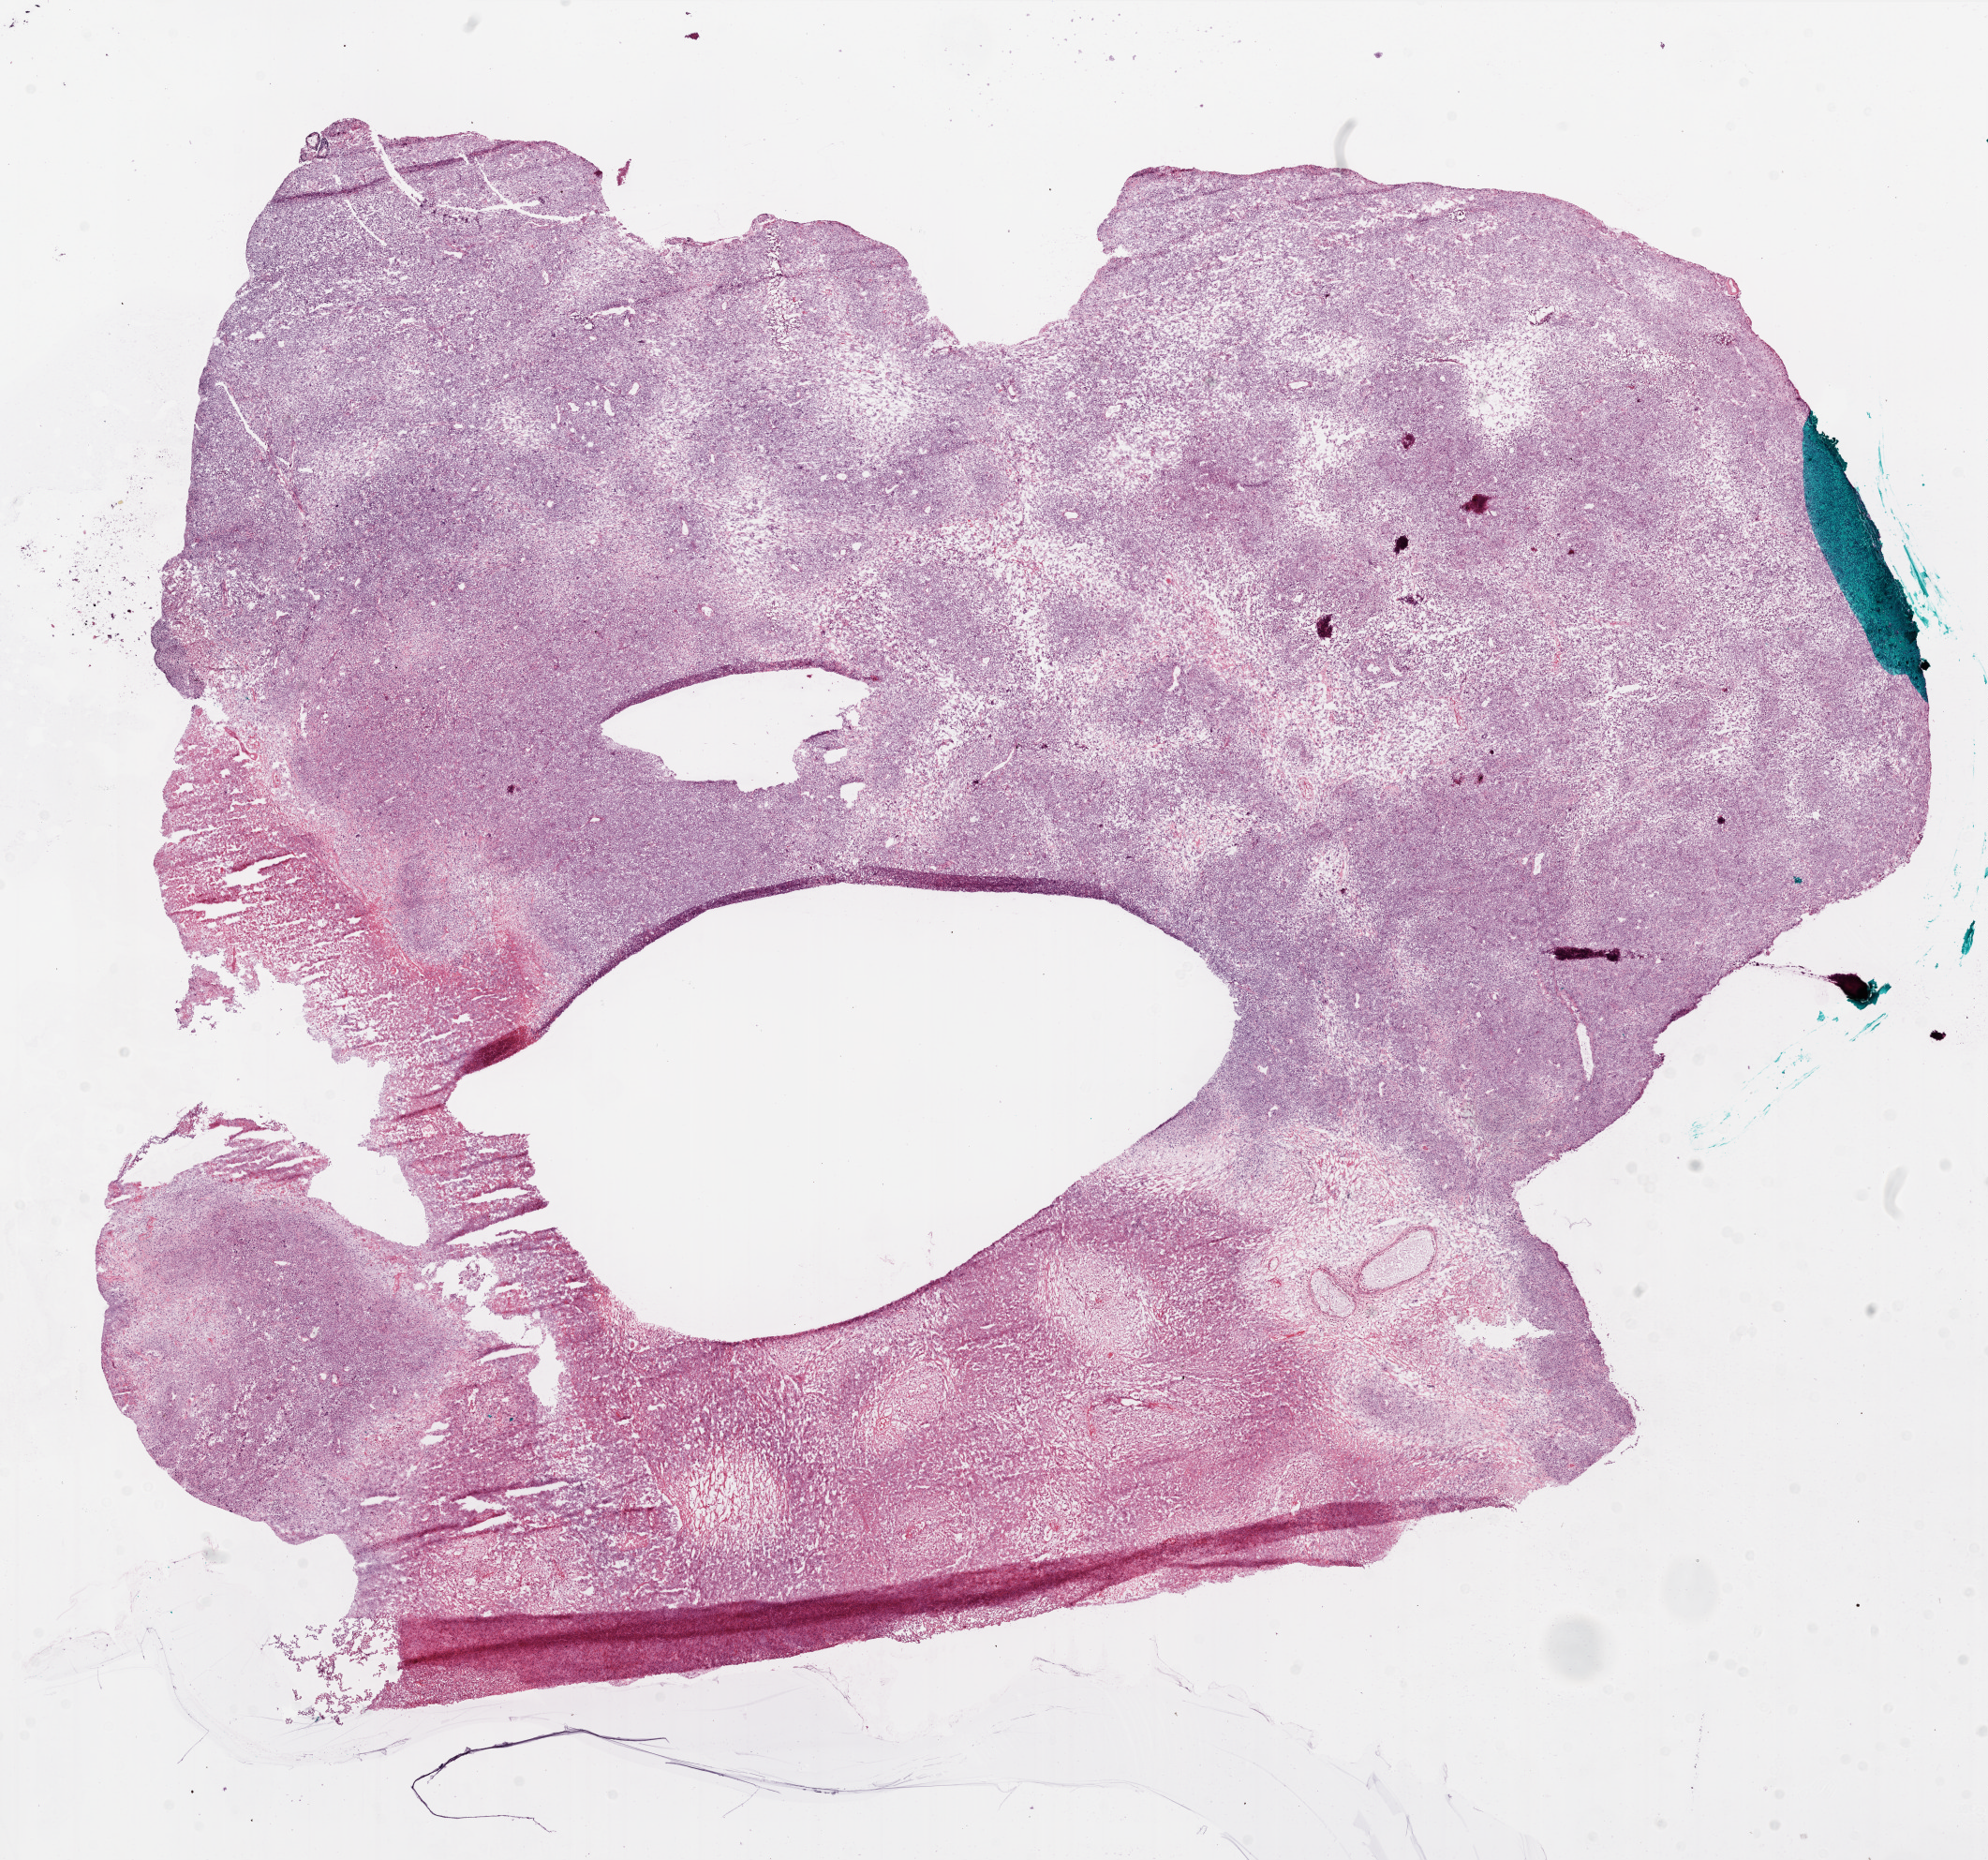
Whole-slide histology image, H&E — whole scanned area (about 17.0 x 15.9 mm) shown as a low-resolution overview, frozen section from the bottom of the tissue portion, sample: primary tumour, brain. Patient: female, age at initial diagnosis 67 years. Slide review estimates, as recorded: tumour cells 50%, tumour nuclei 100%, normal cells 0%, stromal cells 0%, necrosis 50%. Inflammatory infiltration, as recorded: lymphocyte infiltration 0%.
Histologic diagnosis: Glioblastoma.